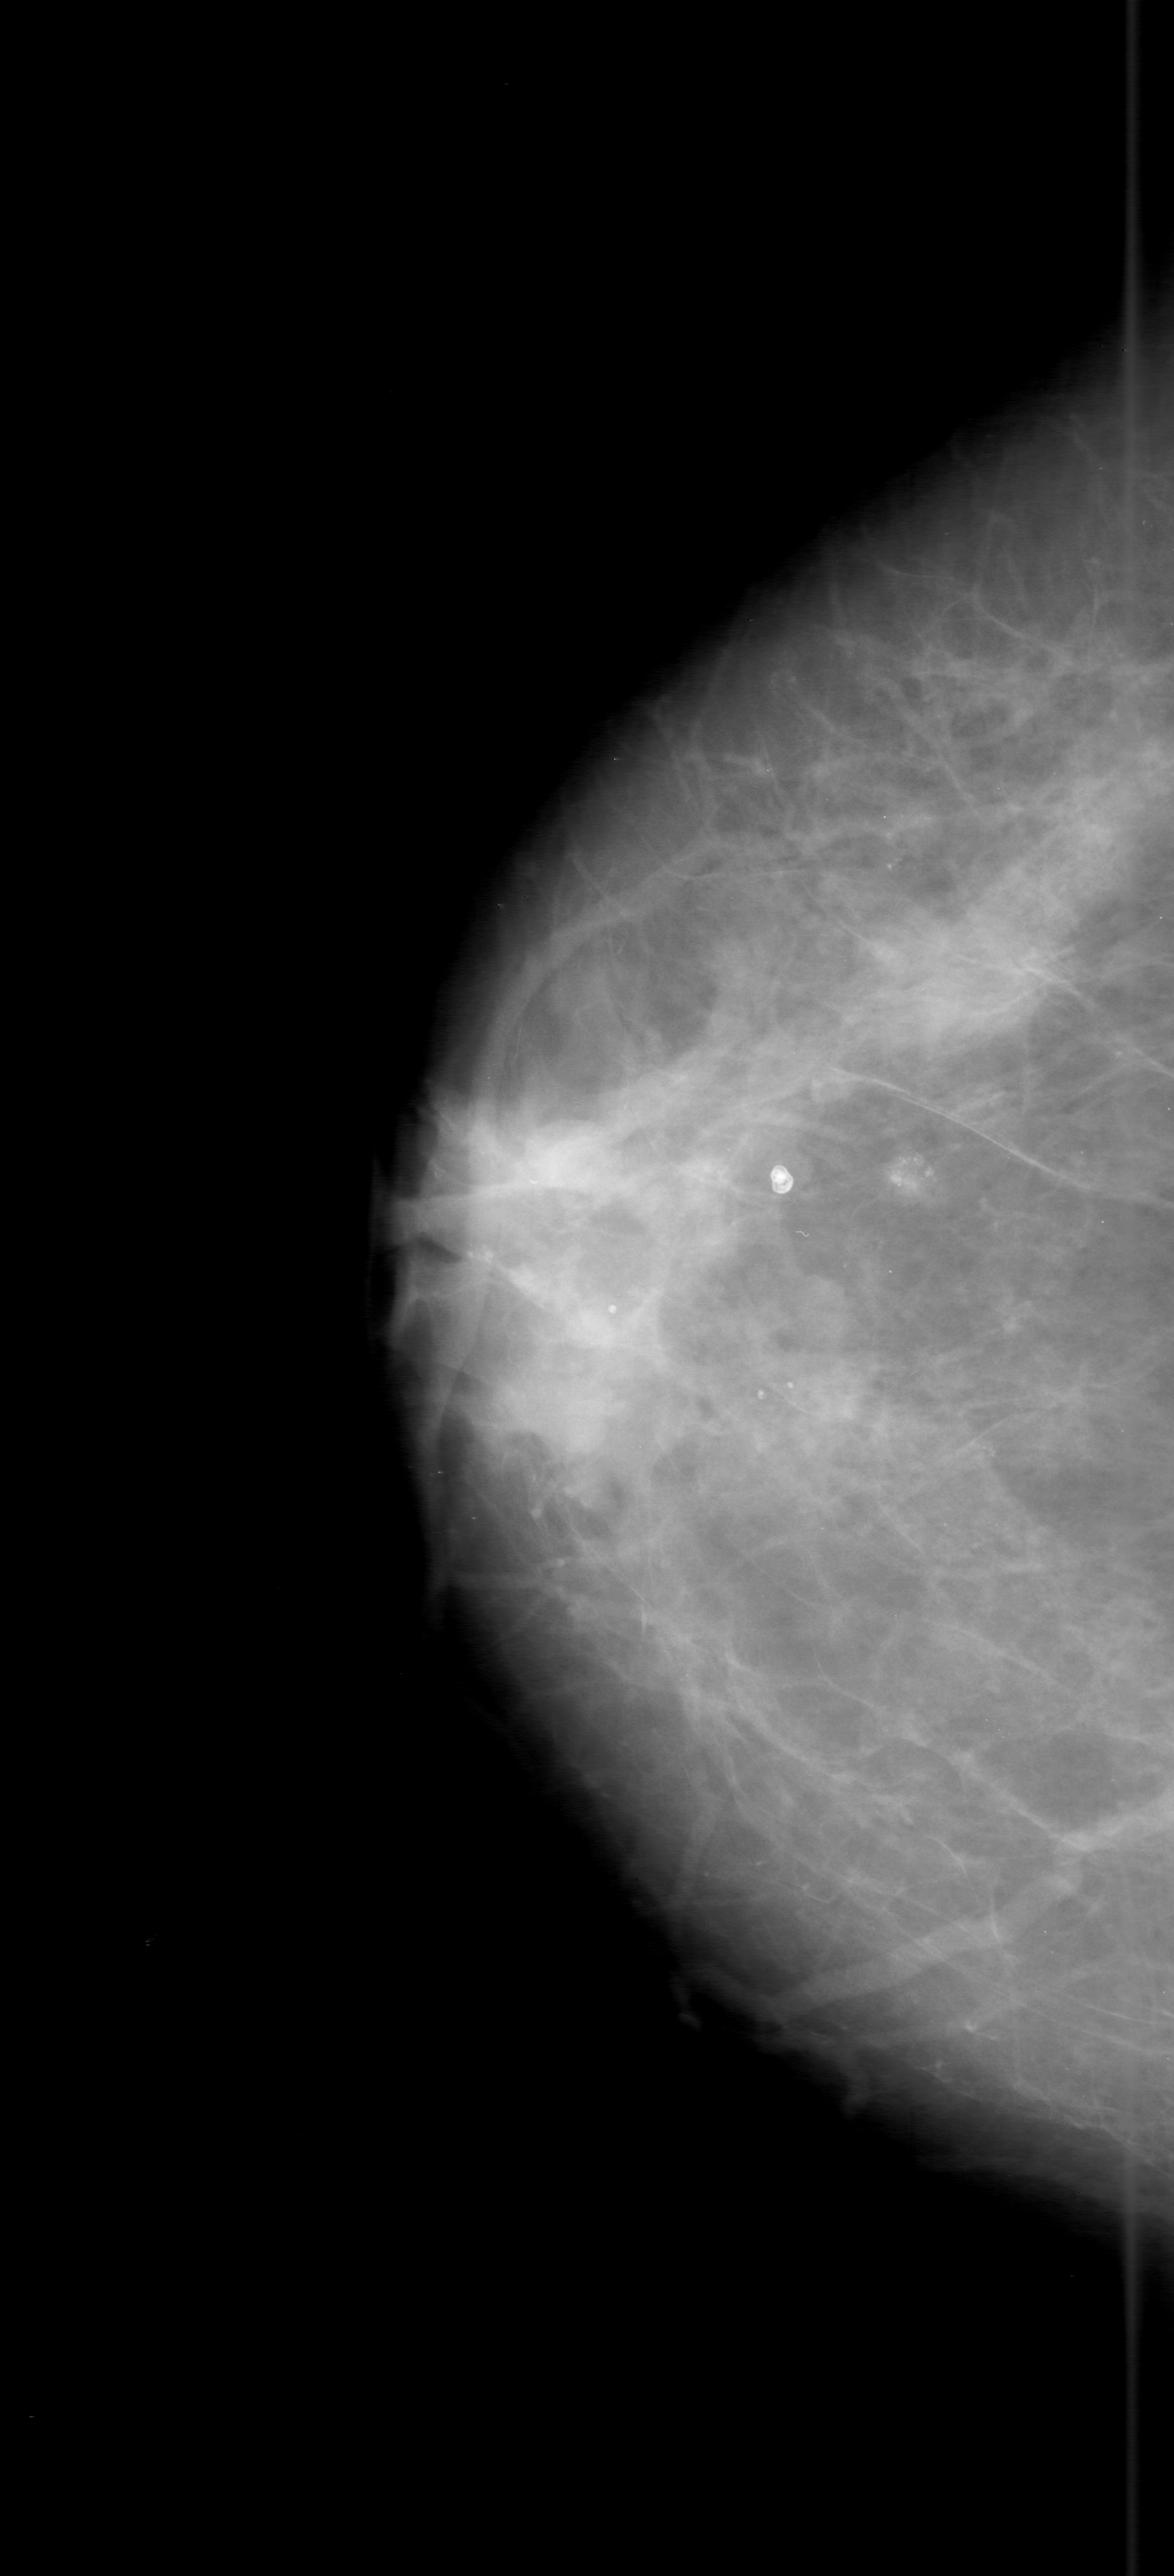
Scanned film-screen mammogram; right breast; CC view; breast composition: scattered fibroglandular densities (BI-RADS density category 2 of 4); 1174 × 2576 image matrix.
Marked abnormalities (boxes around the expert regions of interest):
- calcifications, morphology amorphous, distribution clustered; BI-RADS assessment category 3; pathology result (as recorded, not read from the image): malignant: bounding box (x1, y1, x2, y2) in pixels: (800, 1026, 1060, 1310)